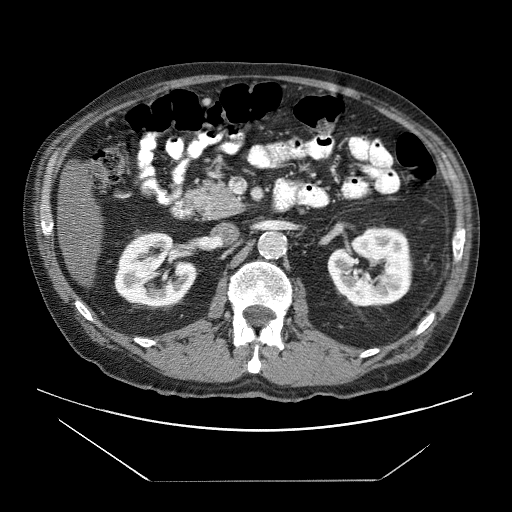
Contrast-enhanced abdominal CT (liver protocol), one axial slice; slice 15 of 83 in the series (ordered by position); 120 kVp; soft-tissue window (W 400 / L 40 HU); 512 × 512 image matrix. Case-level facts recorded for this patient, not image findings: diagnosis: hepatocellular carcinoma (patient treated with transarterial chemoembolisation; whether this scan precedes or follows treatment is not stated here); TNM stage (as recorded): Stage-IVB; Child-Pugh class: B.
Outlined on this slice (semi-automatic segmentation, software-assisted and operator-edited):
- liver parenchyma outside the tumour (the mass and vessels are separate outlines, so this box may not span the whole liver): bounding box (x1, y1, x2, y2) in pixels: (58, 194, 104, 286)